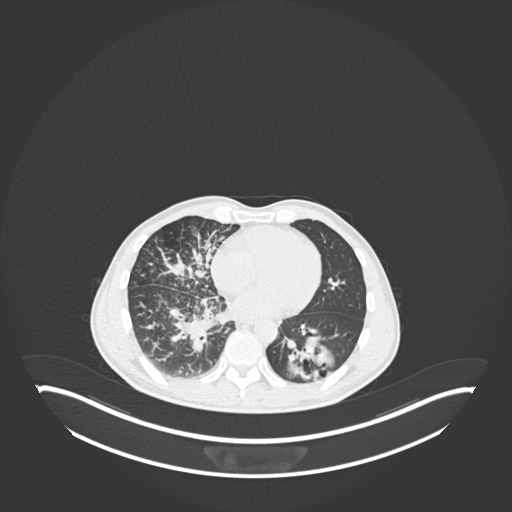
Chest CT, one axial slice. Lung window (W 1500 / L -600 HU). 1 mm slice thickness. 512 × 512 image matrix, field of view 500 × 500 mm. Male patient, age 49 years. From the clinical record (not read from this slice): clinical TNM (as recorded): T2b N1 M0.
Outlined on this slice (rectangle marked by the reading radiologist):
- lung tumour (recorded histology: adenocarcinoma): box from (x=283, y=331) to (x=337, y=385) px